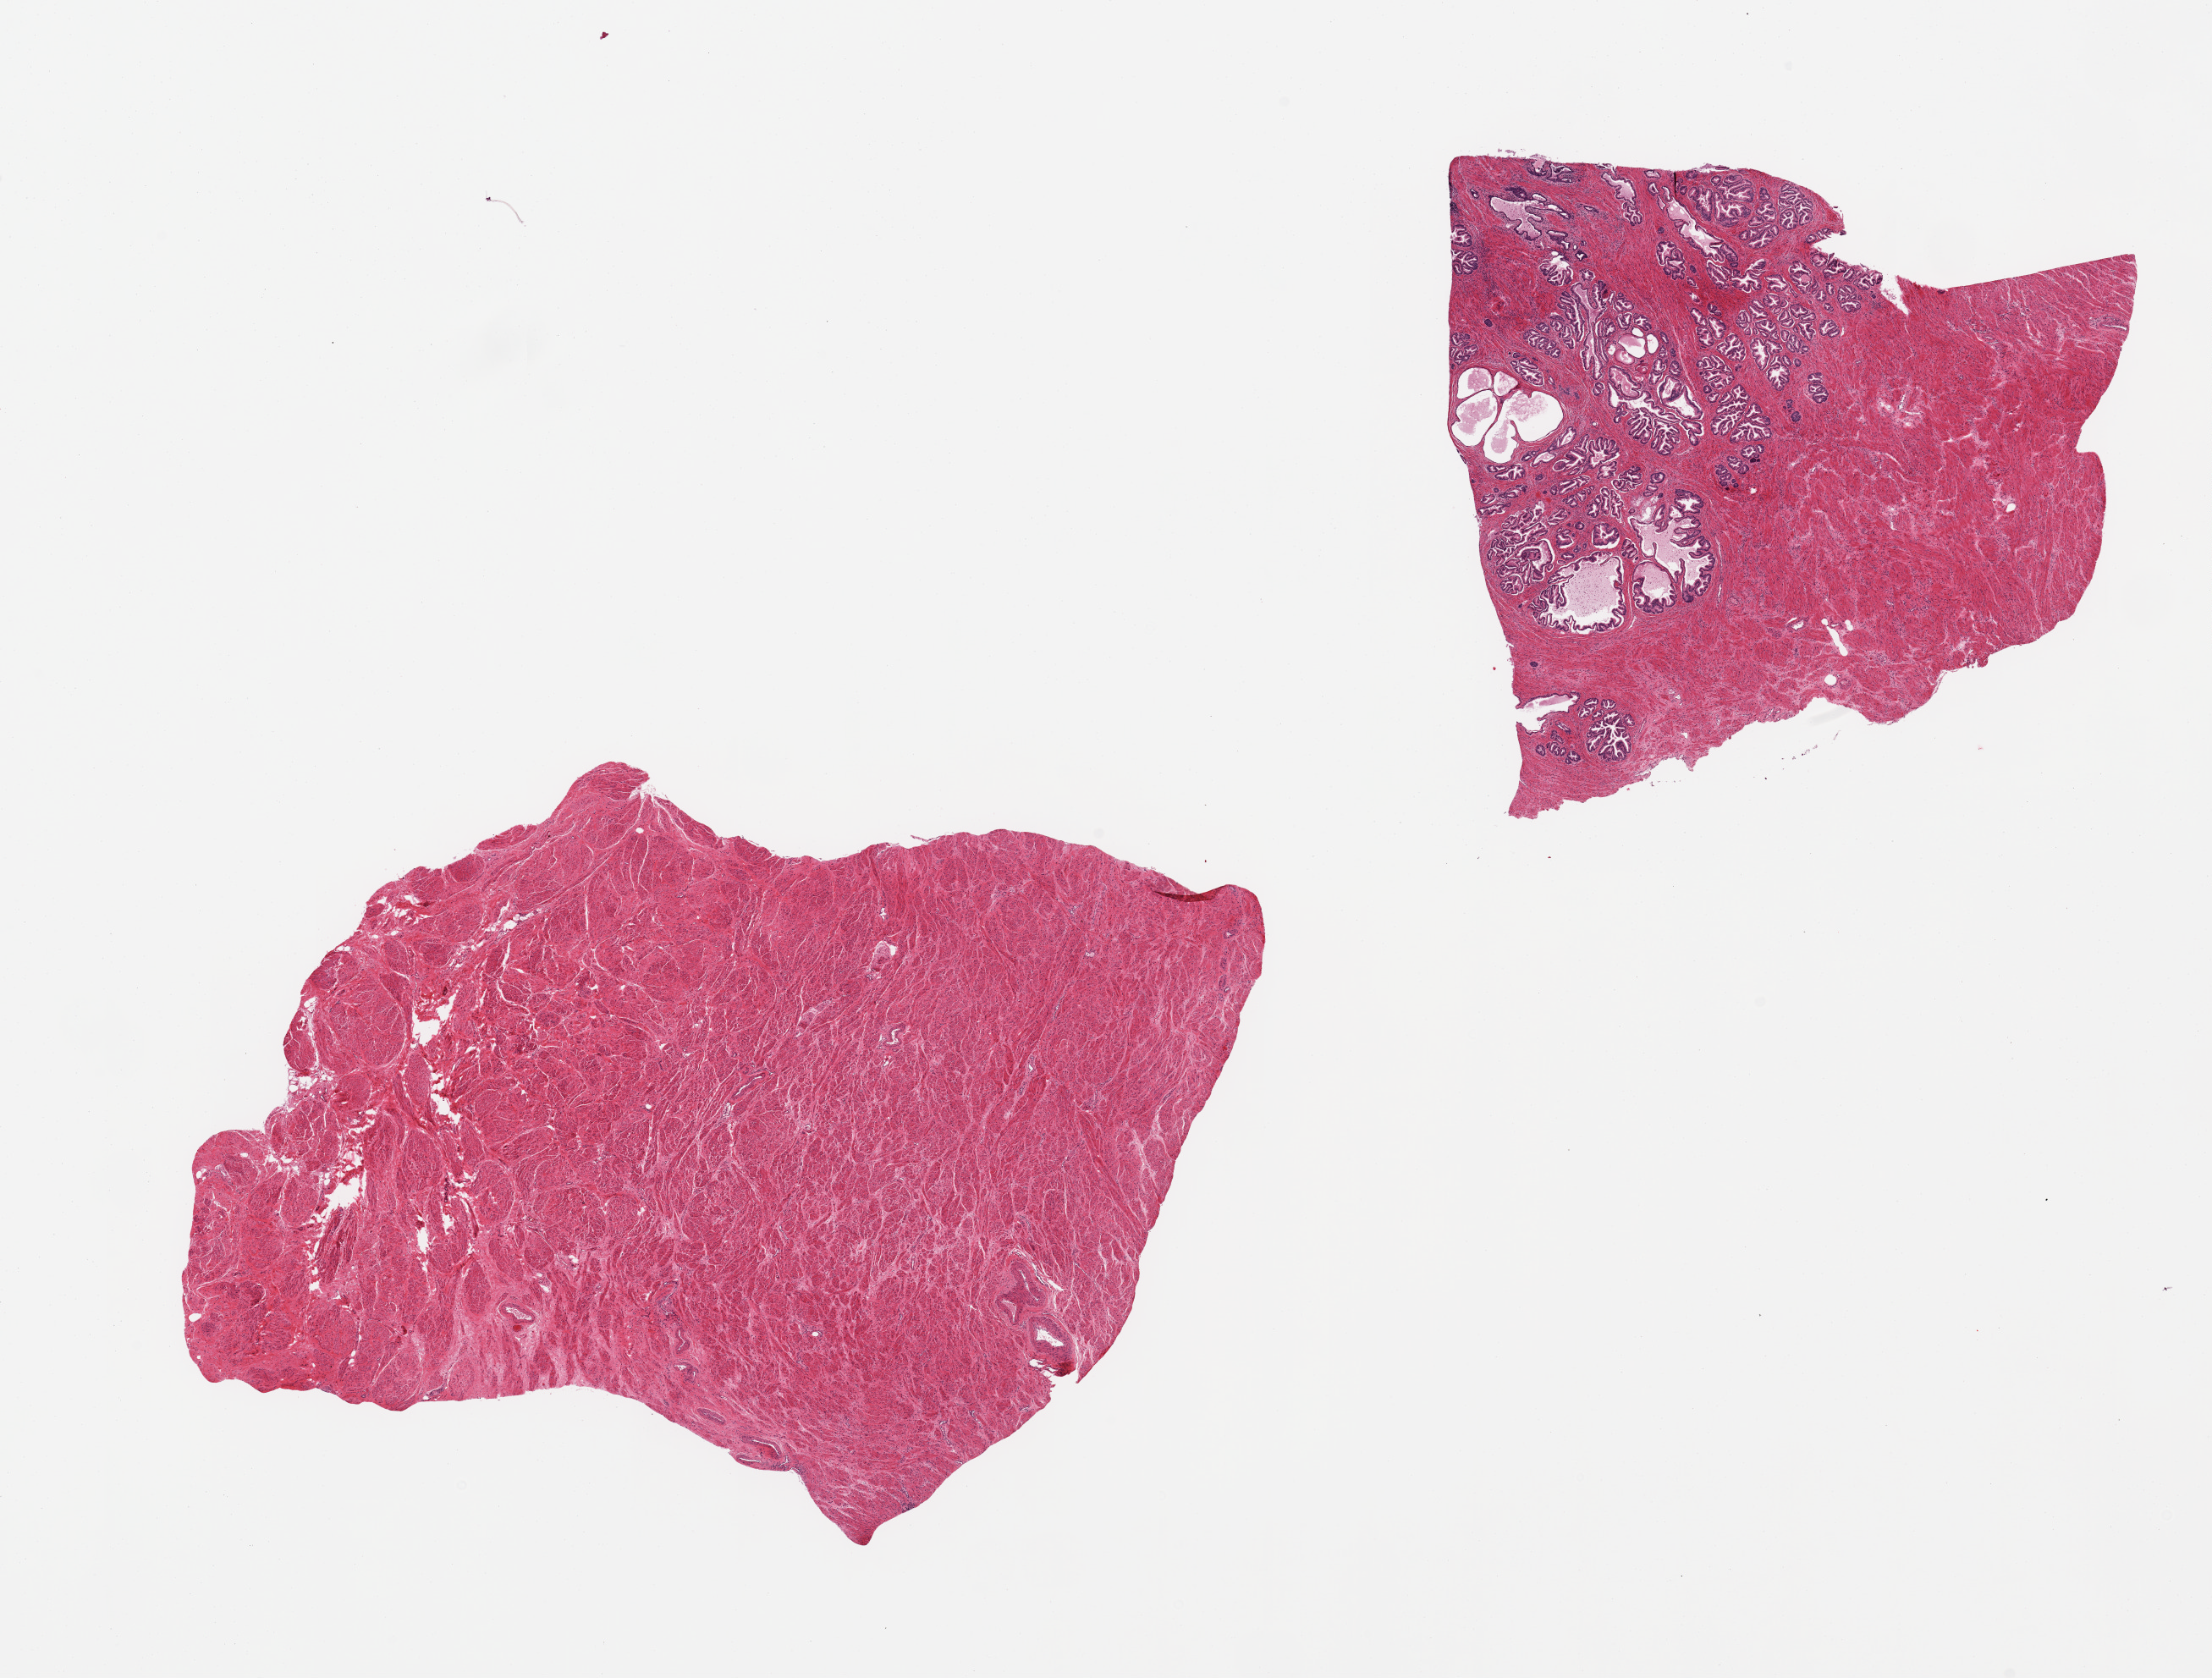
Haematoxylin and eosin whole-slide image, low-resolution overview of the scanned area, about 20.7 x 15.7 mm (from a 20x scan), PAXgene-fixed, paraffin-embedded tissue, sampled site (target tissue): prostate, donor tissue sample. Donor sex: male.
* pathologist's review note for this sample: 2 pieces, no abnormalities